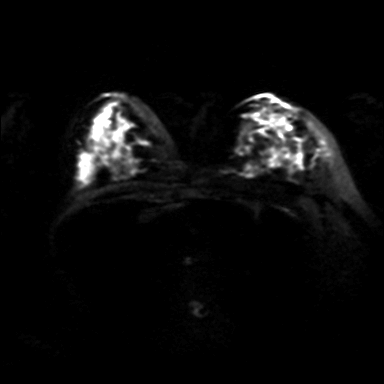
Breast MRI, one axial slice. Position 23 of 36 along the scan axis. Diffusion-weighted series; image 2 of 4 stored at this slice position (different b-values; order by instance number). 3 T. 4 mm slice thickness. 384 × 384 image matrix. Female patient.
Outlined on this slice (expert manual segmentation):
- tumour on diffusion-weighted imaging: bounding box [x1, y1, x2, y2] px = [244, 112, 291, 172]